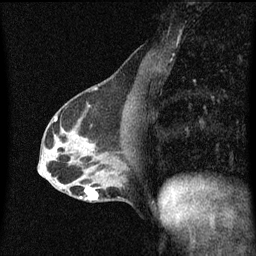
Breast MRI (dynamic contrast-enhanced), one sagittal slice. Position 25 of 60 along the scan axis. Dynamic contrast-enhanced series, image 2 of 3 at this slice position (ordered by acquisition). 1.5 T. TE 4.2 ms, TR 8.4 ms. 2 mm slice thickness. 256 × 256 image matrix, field of view 200 × 200 mm. Female patient, age 40 years.
Structures marked on this image (semi-automatic segmentation, software-assisted and operator-edited):
- analysis volume of interest (the breast-tissue region the enhancement analysis was run in; not a lesion): bounding box (x1, y1, x2, y2) in pixels: (78, 166, 120, 203)
- tumour enhancement mask (voxels above the 70 % enhancement threshold inside the analysis volume of interest): (81, 188, 99, 201)